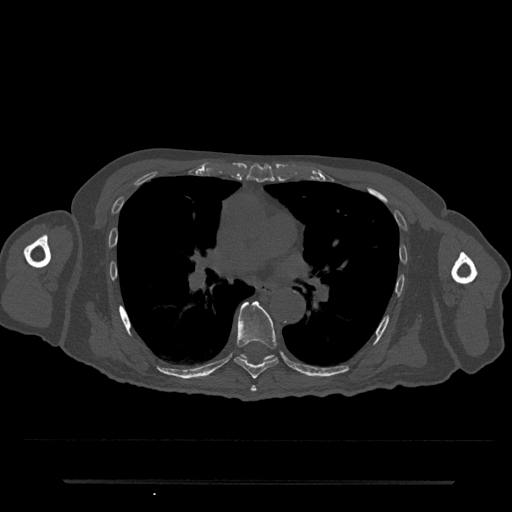
CT including the spine, one axial slice. Position 470 of 797 along the scan axis. Reconstruction kernel Br40s/3. 120 kVp. Bone window (W 1800 / L 400 HU). 0.5 mm slice thickness. 512 × 512 image matrix. Patient: male, 74 years. Case-level facts recorded for this patient, not image findings: primary cancer: prostate.
Structures marked on this image (semi-automatically segmented with operator editing):
- T6 vertebra: bounding box [x1, y1, x2, y2] px = [250, 386, 256, 392]
- T7 vertebra: [234, 301, 279, 379]
- T8 vertebra: [240, 354, 275, 362]